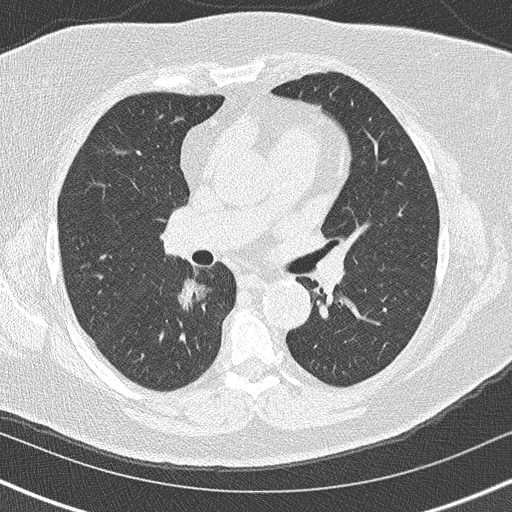
Low-dose screening chest CT, axial slice. Second screening round (one year after baseline). Lung window (W 1500 / L -600 HU). Lung (sharp) reconstruction kernel (B50f). Female, age 60 years at enrolment. Former smoker at enrolment.
• Lesion marked by an expert reader, bounding box <150,265,214,322> (left, top, right, bottom; pixels).
• The exam's reader record, not a measurement of the box and not confirmed to be the same lesion: non-calcified nodule or mass ≥4 mm, right lower lobe, 20 × 19 mm, soft tissue attenuation, pre-existing on the prior screen: yes; interval growth: yes.
• Official screen result: positive, other.